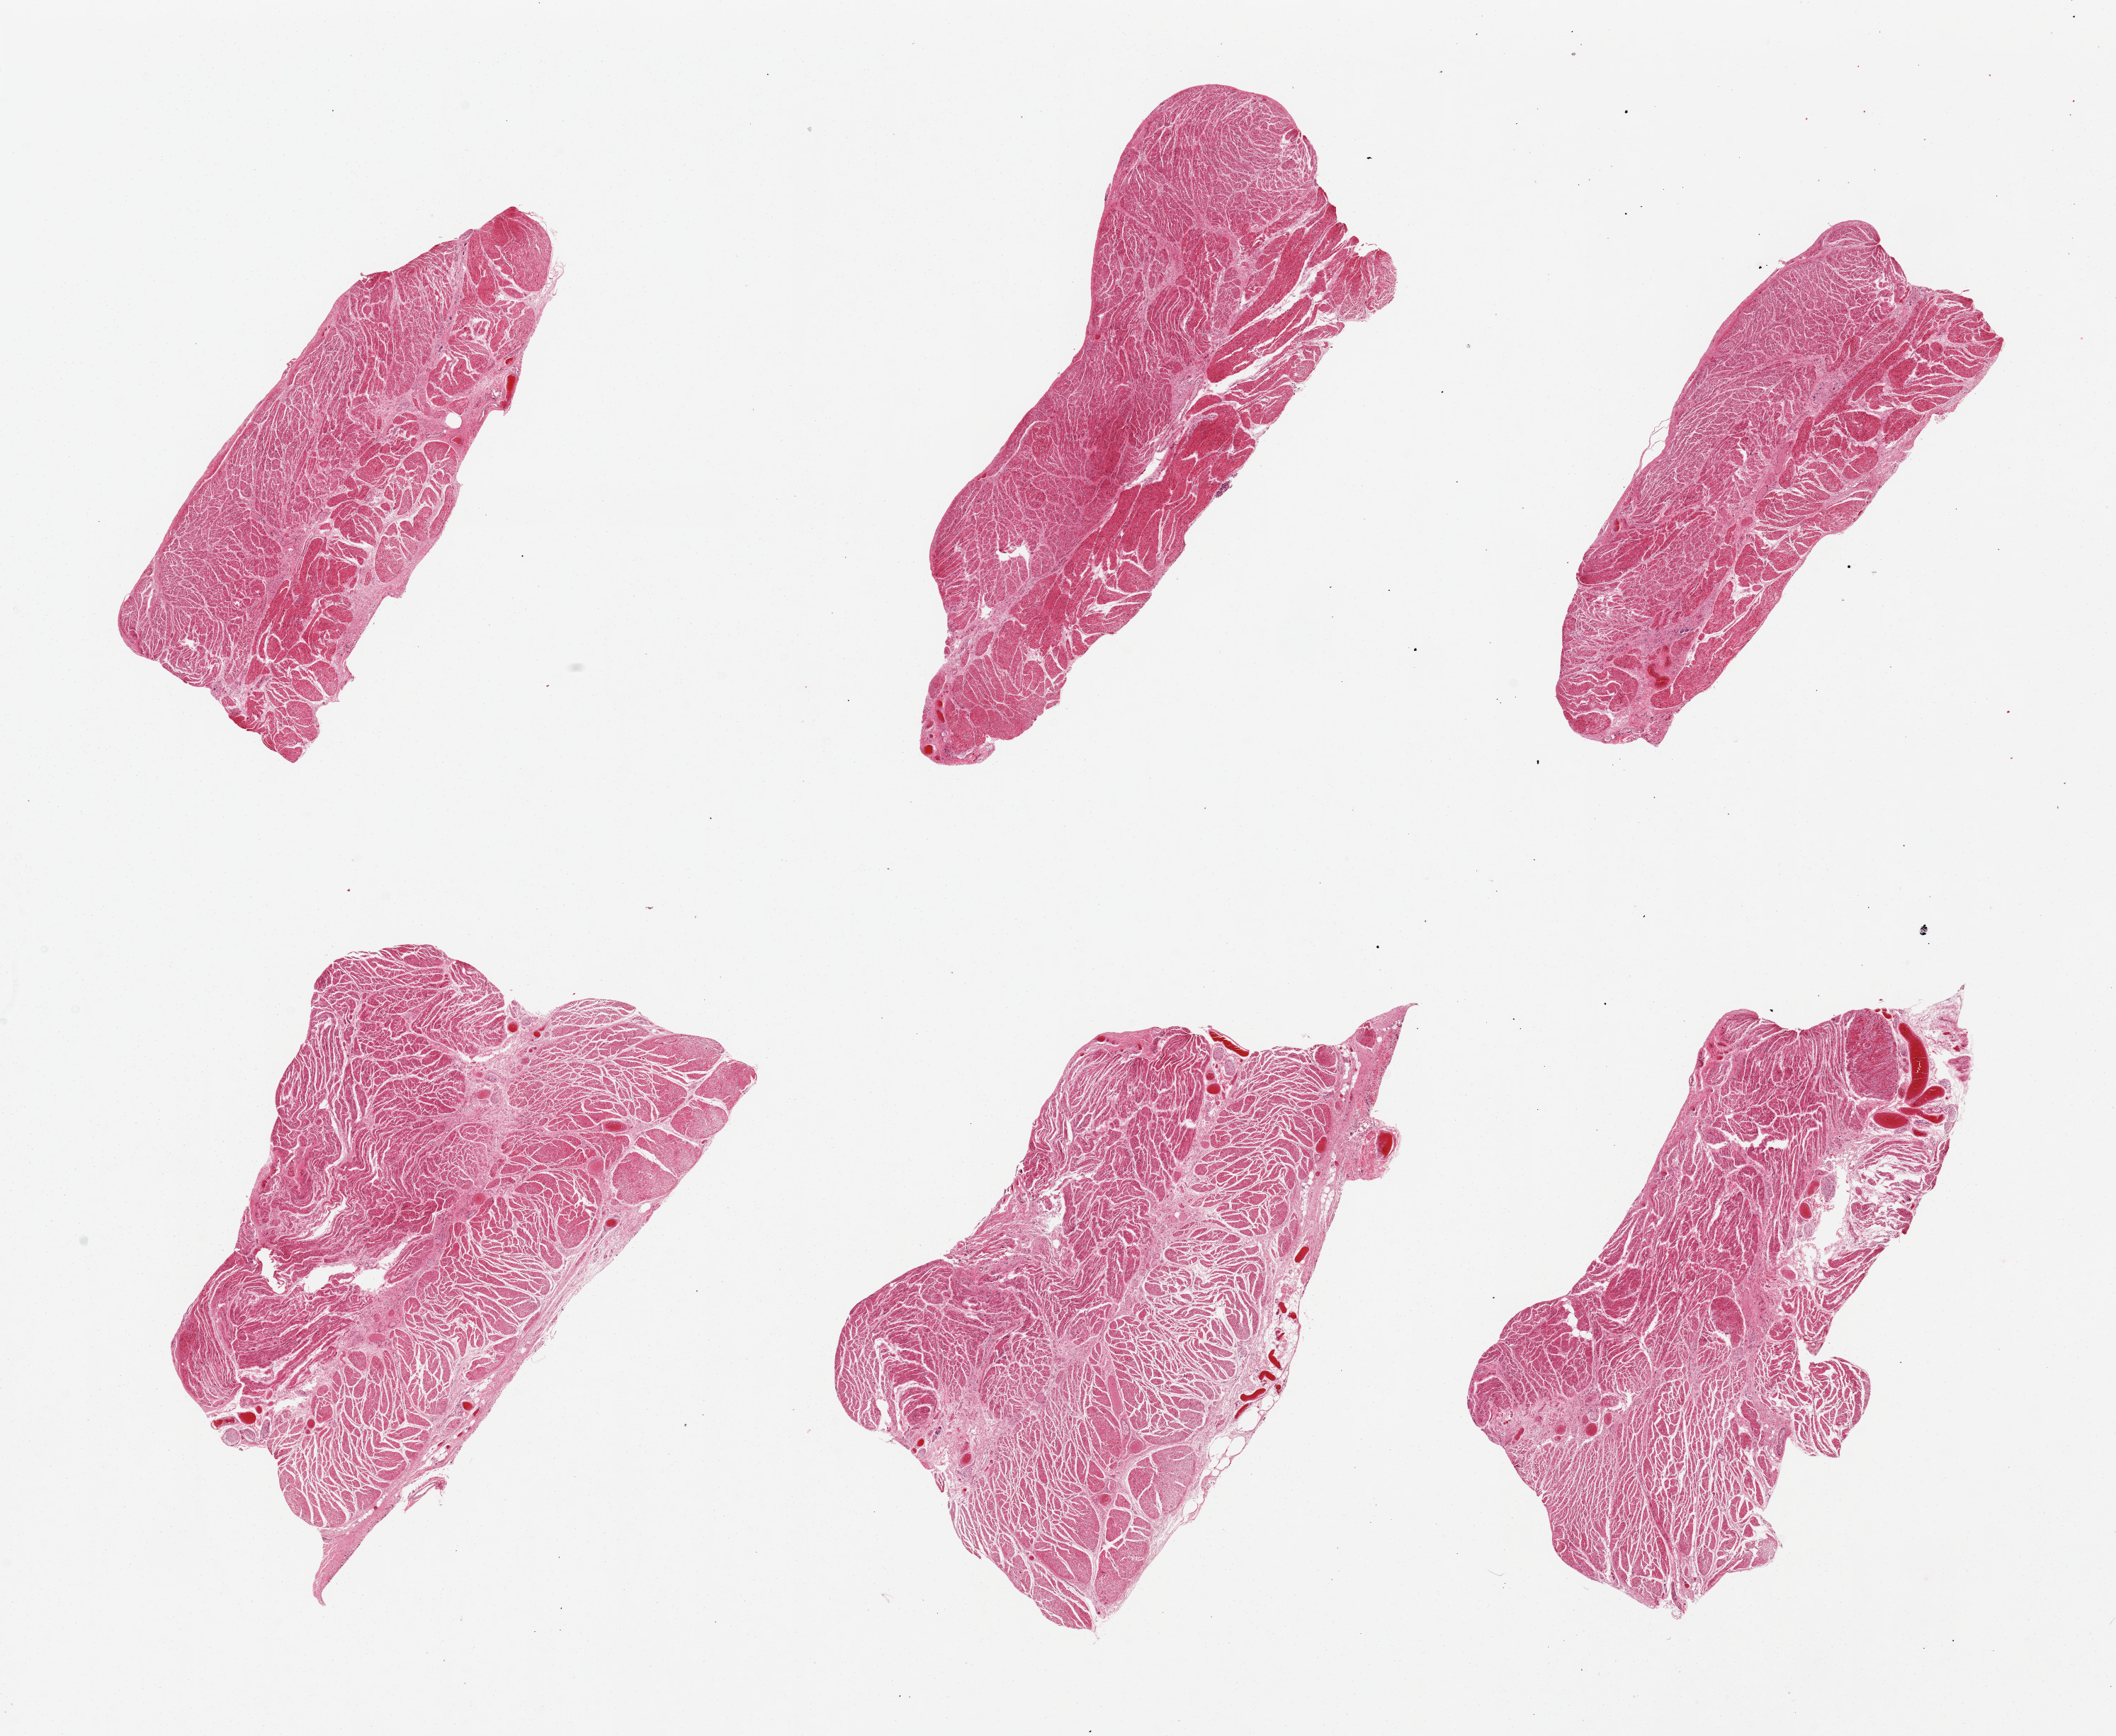
Haematoxylin and eosin whole-slide image — low-resolution overview of the scanned area, about 23.6 x 19.4 mm (slide scanned at 20x). PAXgene-fixed paraffin-embedded (PFPE) section. Target tissue: gastroesophageal junction. Donor tissue sample. Donor: female.
- pathologist's review note for this sample: 6 pieces, all muscularis, good specimens